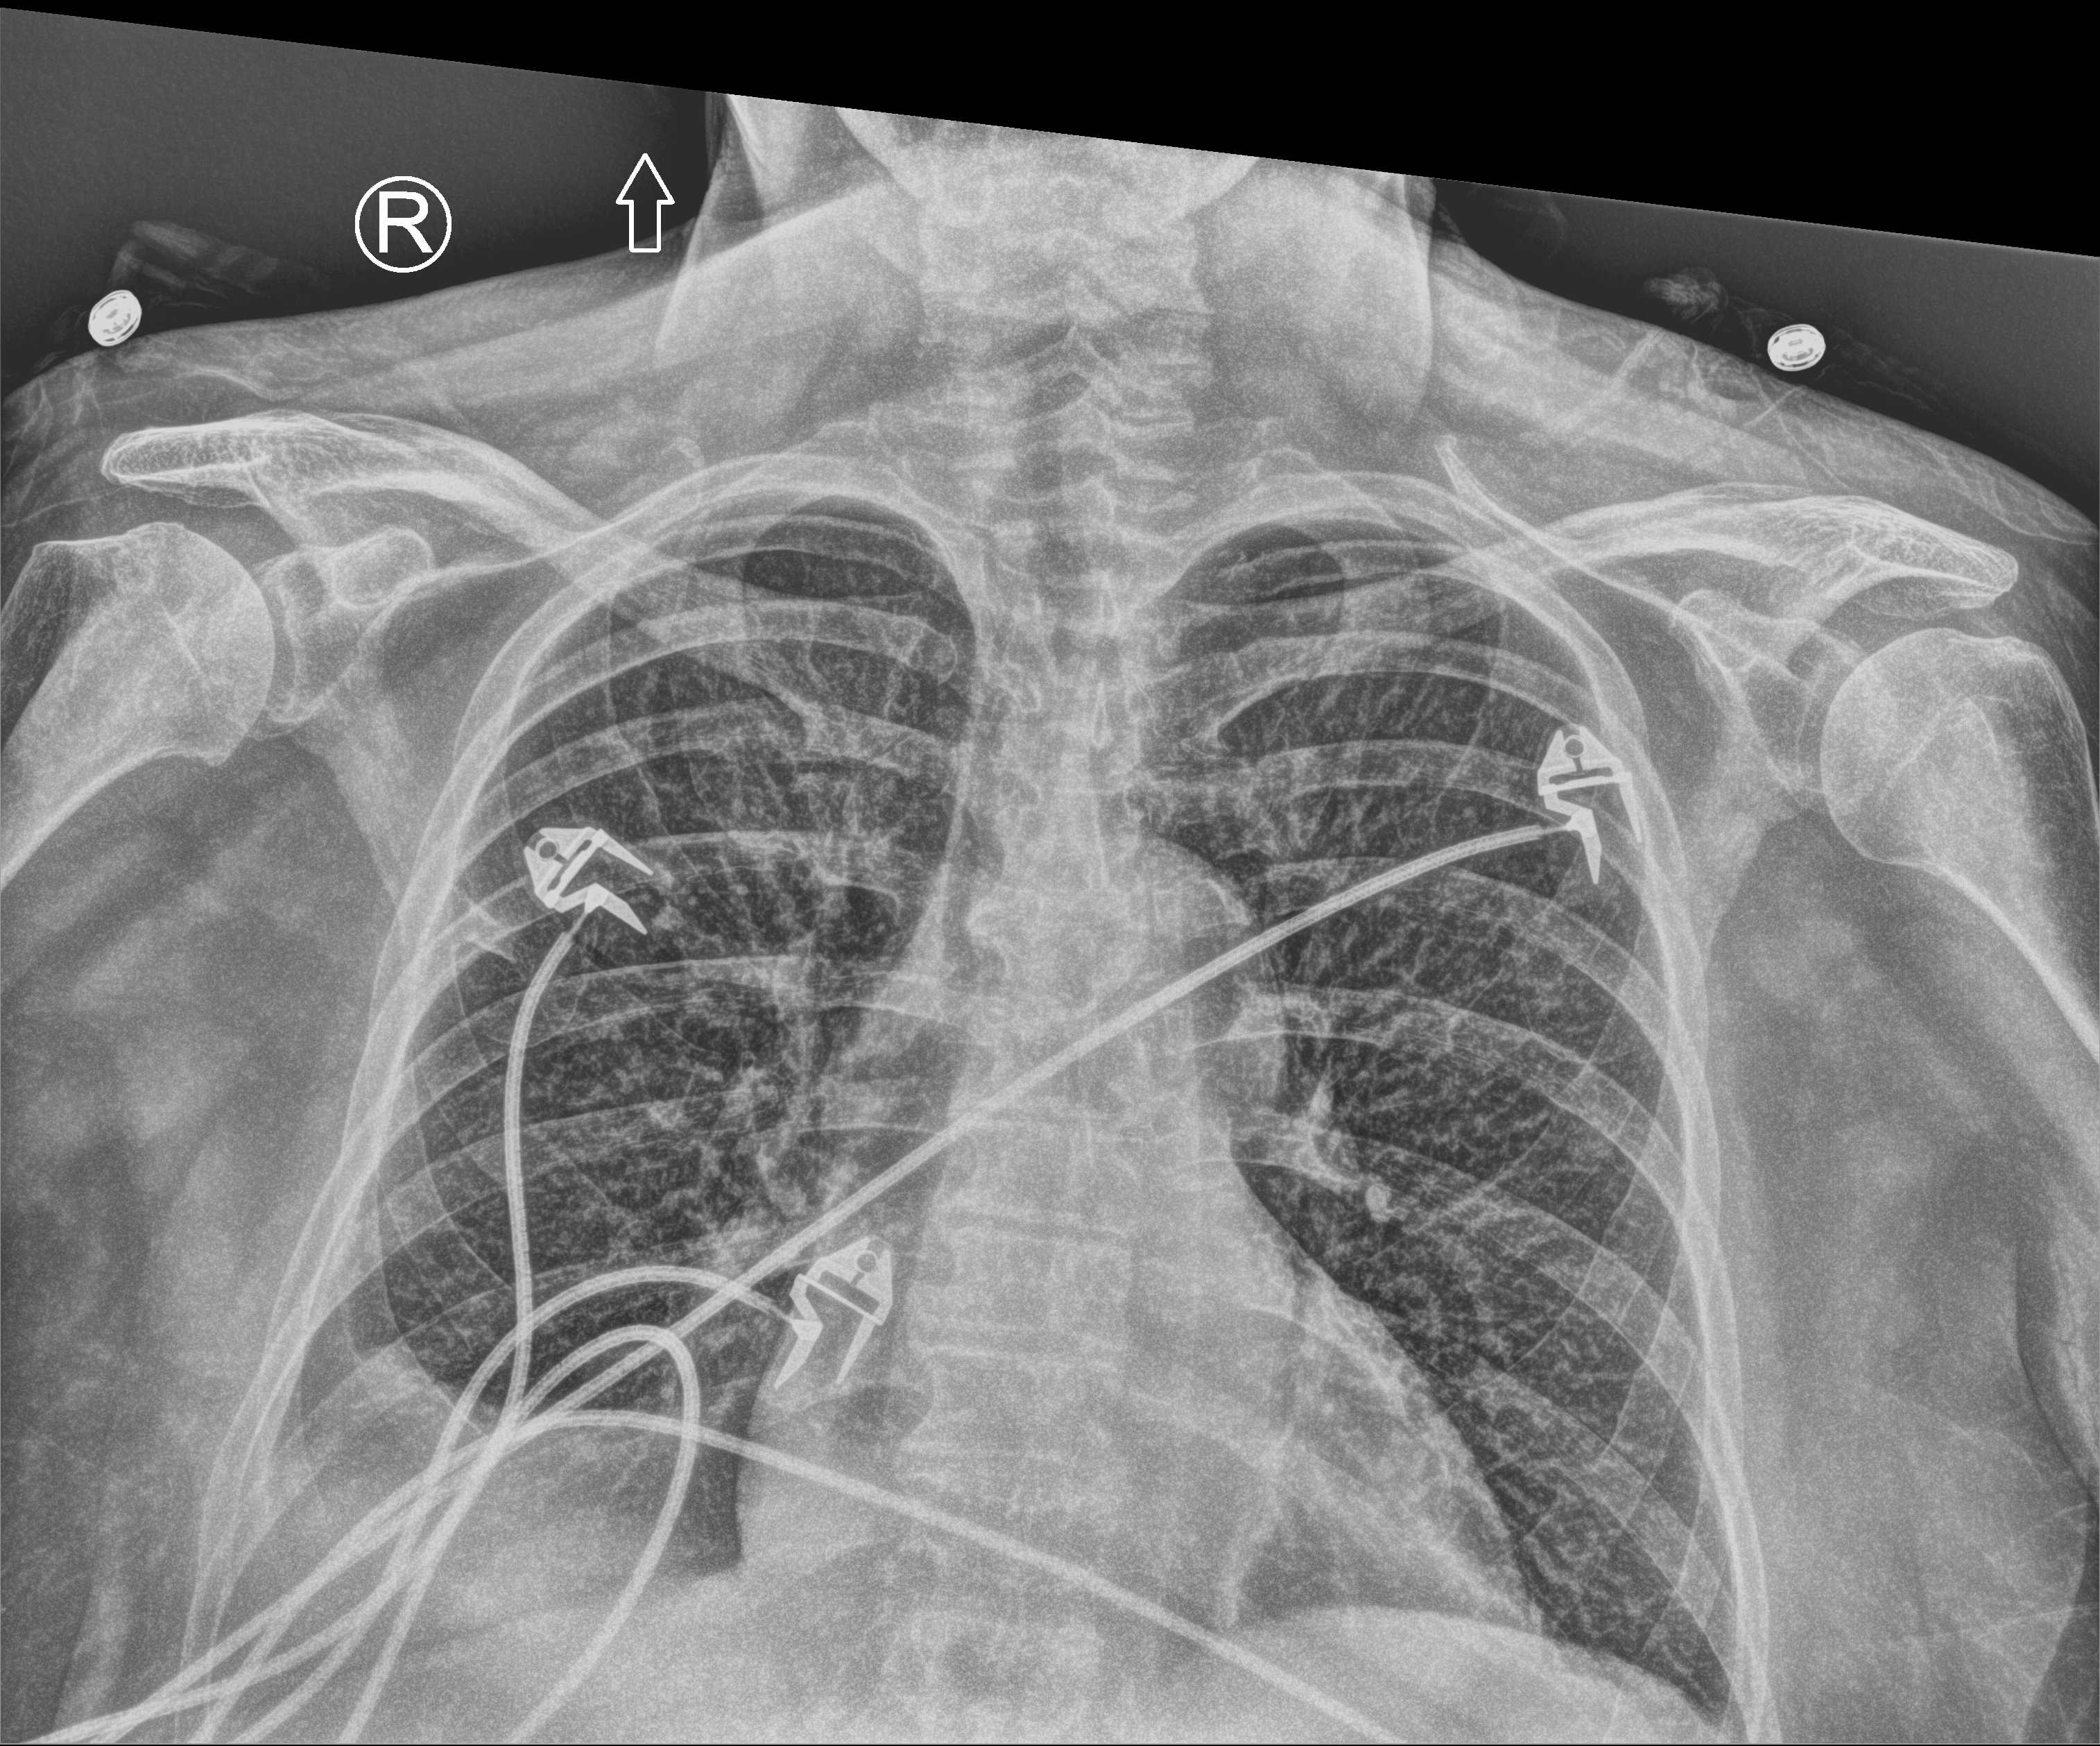
Bedside chest radiograph (computed radiography); anteroposterior (AP) projection. Patient hospitalised with COVID-19; female, aged 75–90 years.
Admission-level facts for this patient (not findings on this image; timing relative to this image not recorded): mechanically ventilated during this hospital stay: no; length of hospital stay: 10 days.